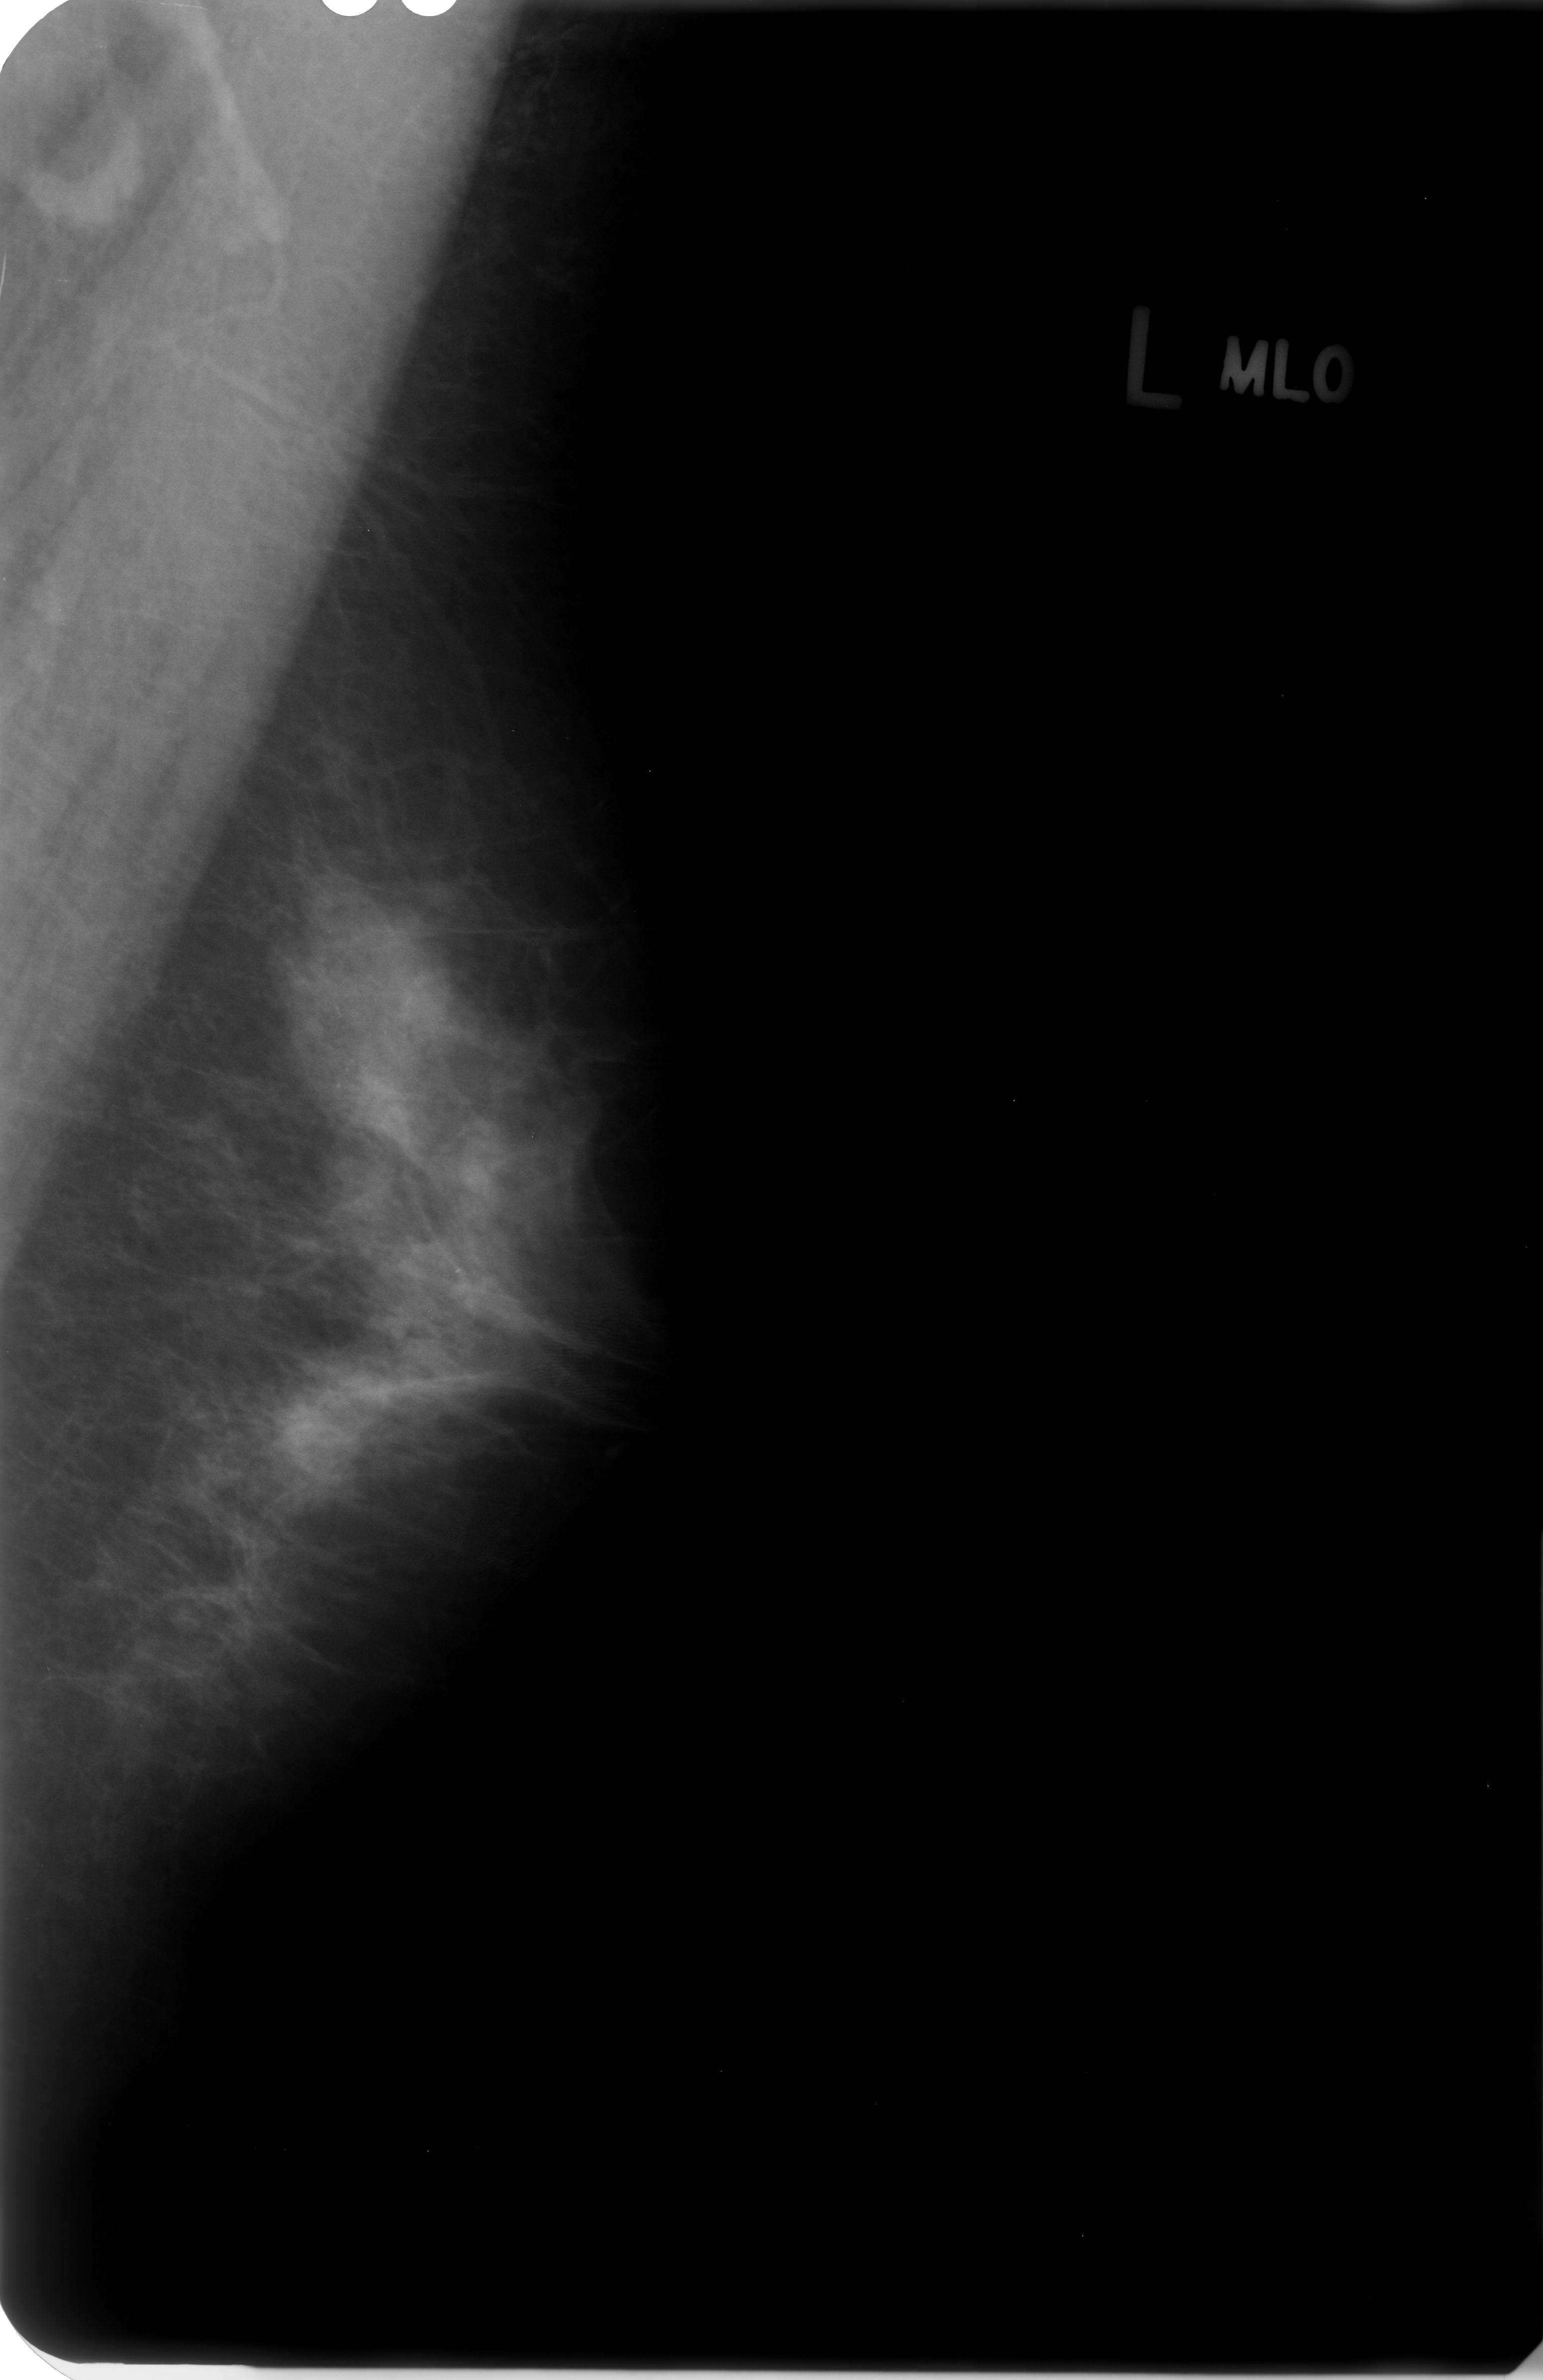
Scanned film-screen mammogram. Left breast. Mediolateral oblique (MLO) view. BI-RADS breast density category 2 (scale 1–4). 1543 × 2380 image matrix.
Expert-marked regions of interest on this image (one box per marked abnormality):
- calcifications, morphology punctate, distribution segmental; BI-RADS assessment category 4; subtlety rating 3 on a 1 (subtle) to 5 (obvious) scale; pathology (as recorded): benign: bounding box (x1, y1, x2, y2) in pixels: (227, 825, 555, 1209)